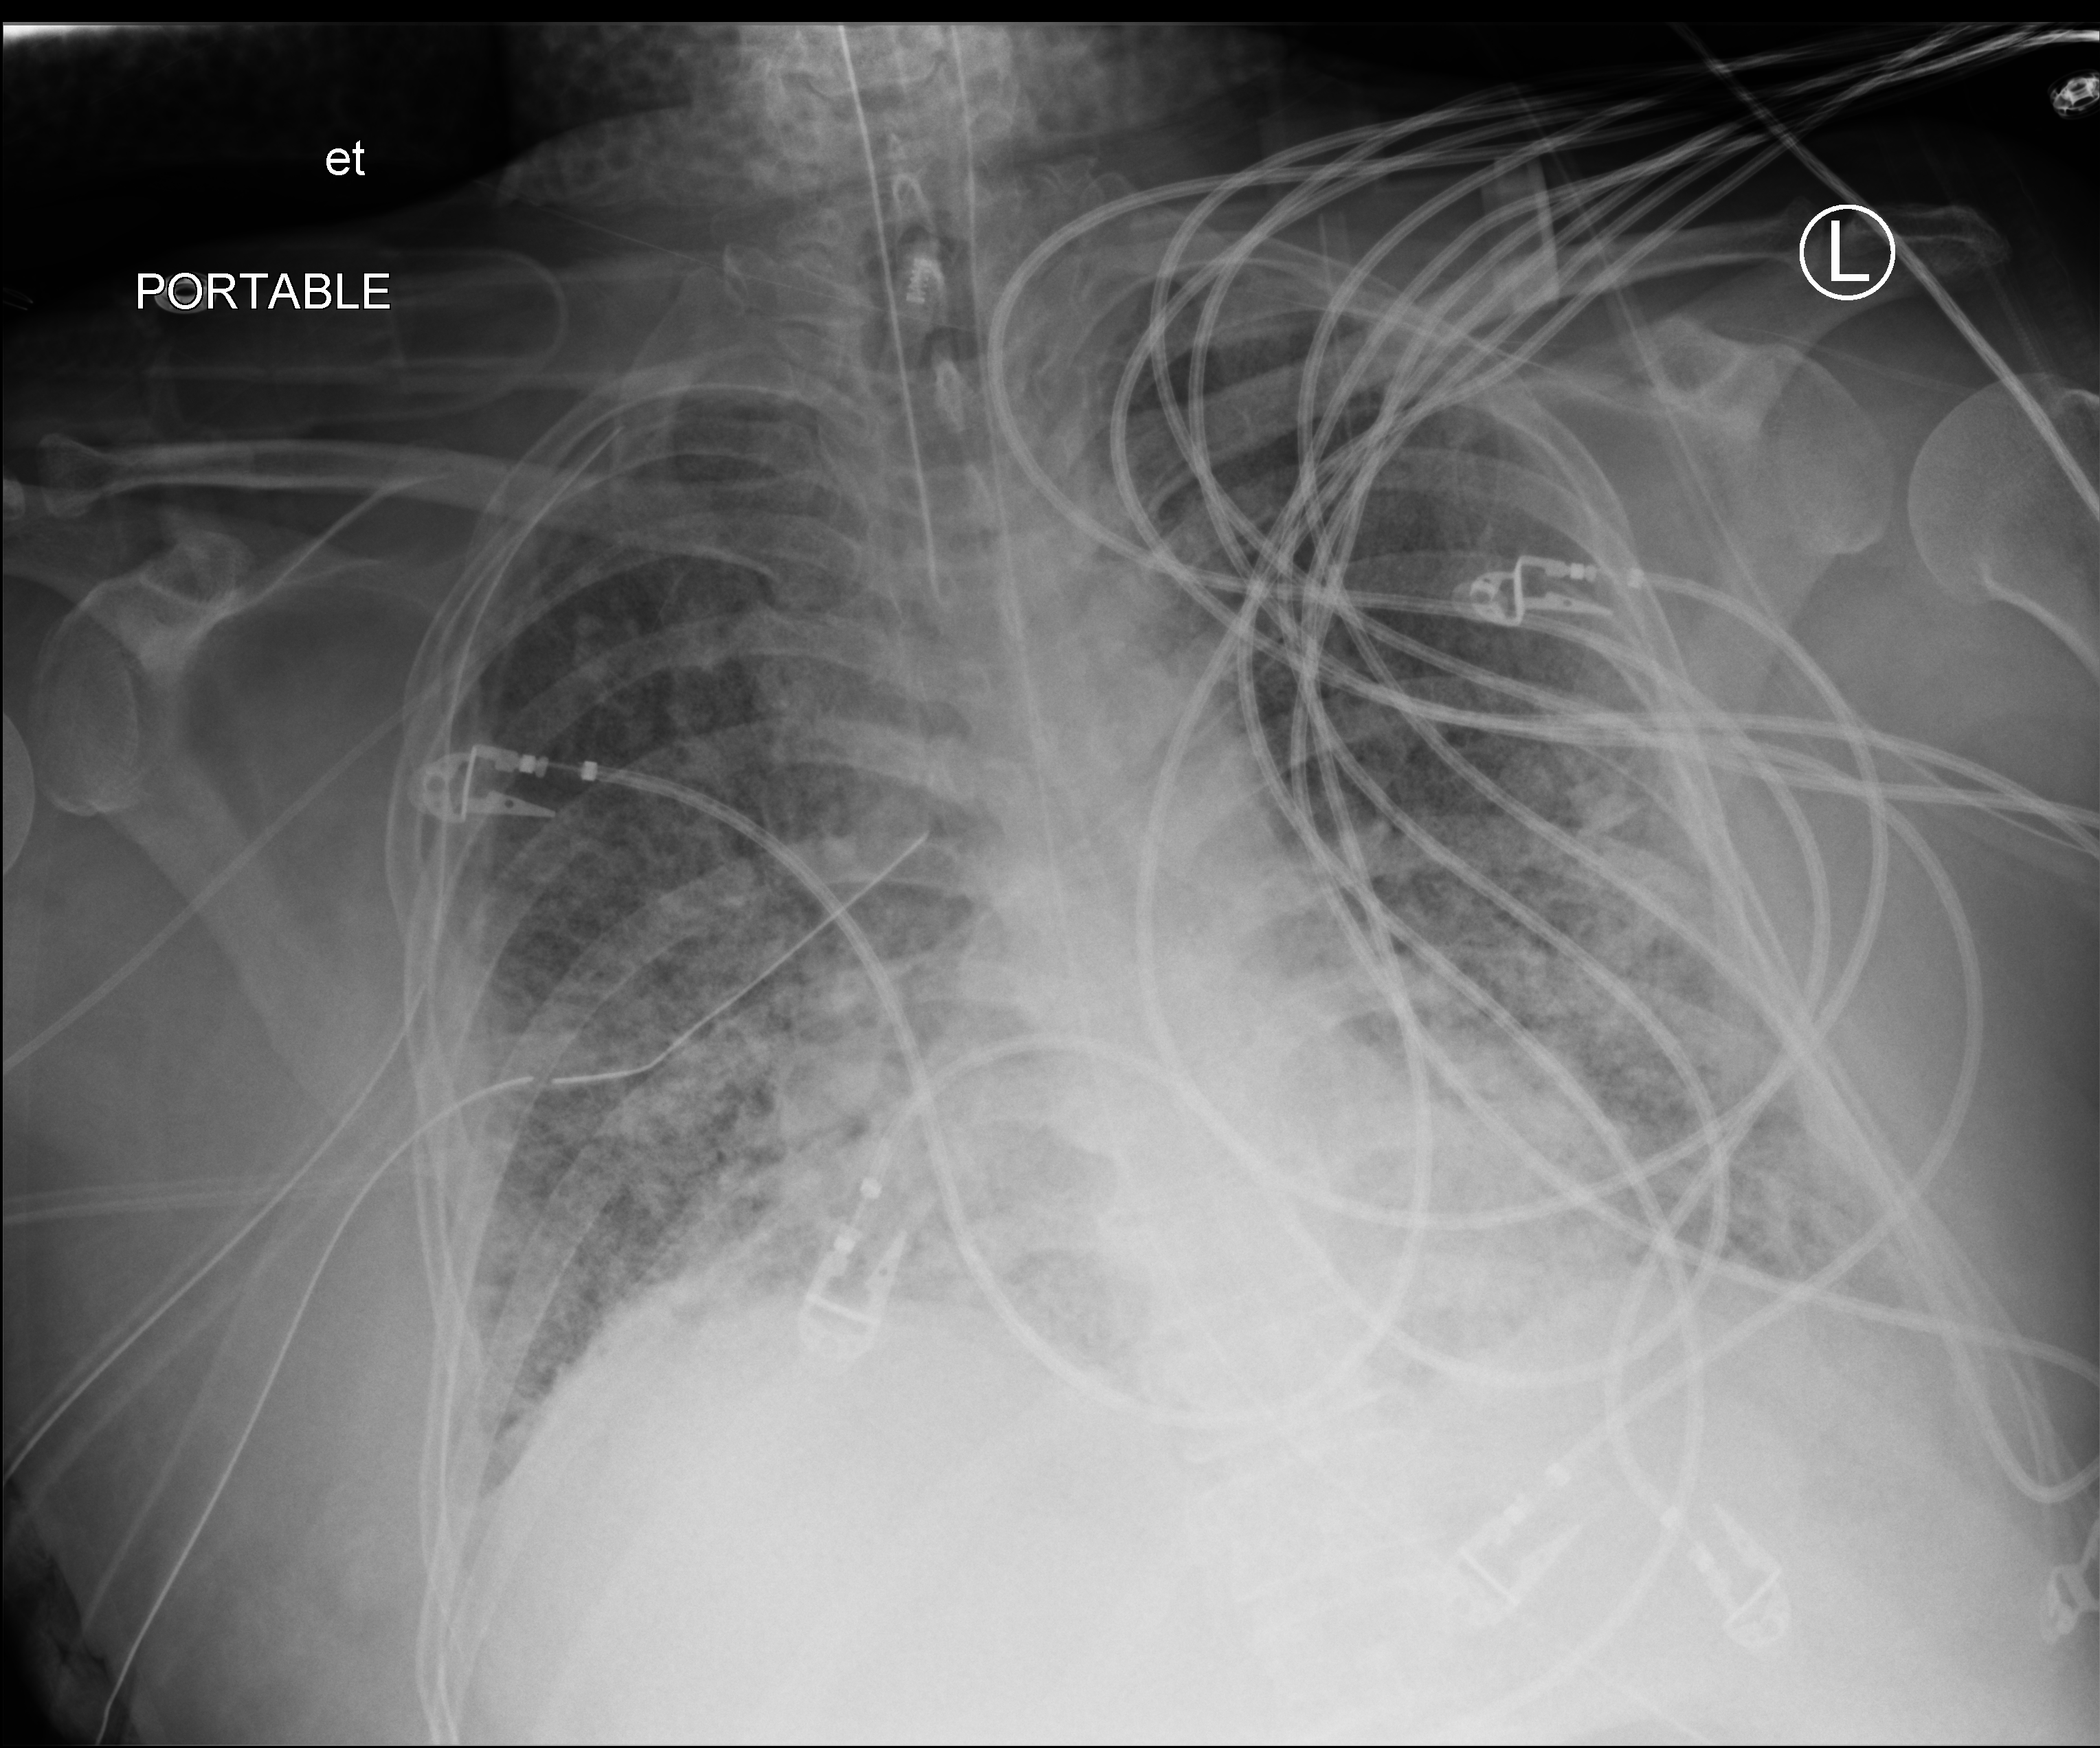
Bedside chest radiograph (computed radiography); anteroposterior (AP) projection. Adult patient hospitalised with COVID-19, age 18–59 years.
From the hospital-stay record, not from the radiograph (when in the stay this image was taken is not recorded): mechanically ventilated during this hospital stay: yes.